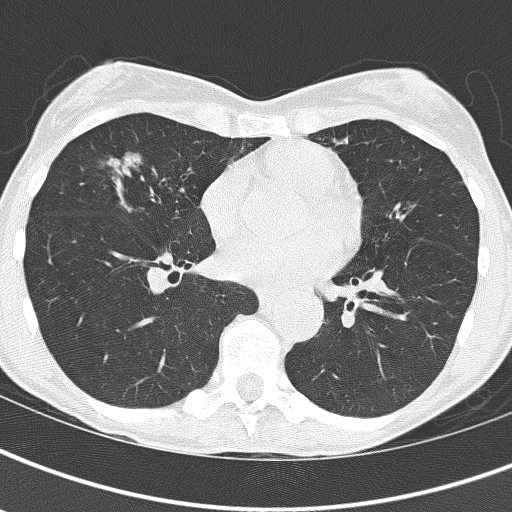
Chest CT (low-dose screening protocol), one axial image. Baseline screening round. Lung window (W 1500 / L -600 HU). 2 mm slice thickness. Lung (sharp) reconstruction kernel (B60f). 120 kVp. Slice 92 of 161 in the series. 512 × 512 image matrix. Female participant, aged 67 years at enrolment.
- Expert-annotated lung lesion, bounding box [x1, y1, x2, y2] px = [89, 135, 176, 215].
- No non-calcified nodule or mass ≥4 mm was recorded by the screening reader at this exam.
- Official screen result: negative screen, significant abnormalities not suspicious for lung cancer.
- Lung cancer was diagnosed 832 days after this screen (after the third annual screen): bronchiolo-alveolar adenocarcinoma, NOS, right middle lobe, well differentiated (G1), stage IA (AJCC 6th edition), 25 mm at pathology.